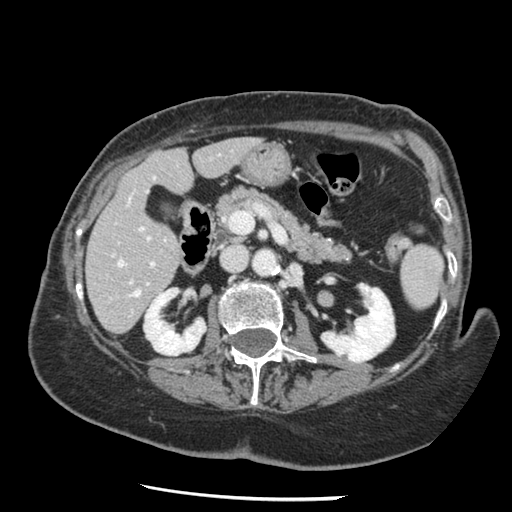
Contrast-enhanced abdominal CT, one axial slice. Slice 61 of 148 in the series (ordered by position). 120 kVp. Intravenous contrast given. Soft-tissue window (W 400 / L 40 HU). 512 × 512 image matrix, field of view 330 × 330 mm. Female patient, age 85 years. From the clinical record (not read from this slice): diagnosis: colorectal cancer liver metastases, imaged before liver resection; multiple liver metastases: no; largest metastasis: 0.9 cm; disease in both lobes: no.
Outlined on this slice (manually delineated by an expert):
- hepatic veins: bounding box (x1, y1, x2, y2) in pixels: (117, 227, 148, 296)
- liver: (86, 138, 257, 333)
- planned liver remnant (the part of the liver to remain after resection): (87, 138, 257, 317)
- portal vein (with intrahepatic branches): (151, 263, 154, 266)